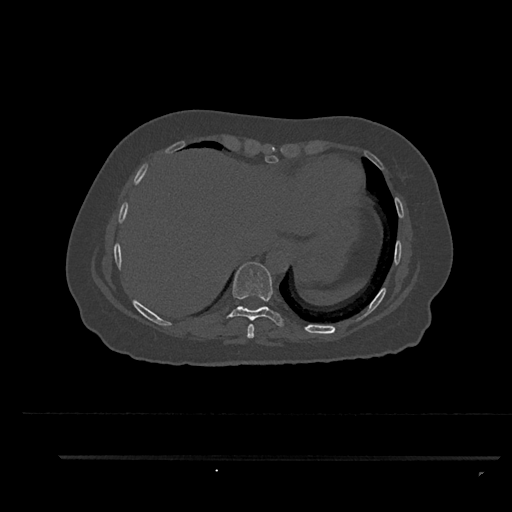
CT including the spine, one axial slice. Slice 415 of 797 in the series (ordered by position). Reconstruction kernel Br40s/3. 120 kVp. Bone window (W 1800 / L 400 HU). 0.5 mm slice thickness. 512 × 512 image matrix. Female patient, age 44 years. Case-level facts recorded for this patient, not image findings: primary cancer: renal; vertebrae with lytic lesions (as recorded): L1.
Structures marked on this image (semi-automatic segmentation, software-assisted and operator-edited):
- T8 vertebra: bounding box <247,324,255,339> (left, top, right, bottom; pixels)
- T9 vertebra: <226,262,284,327>